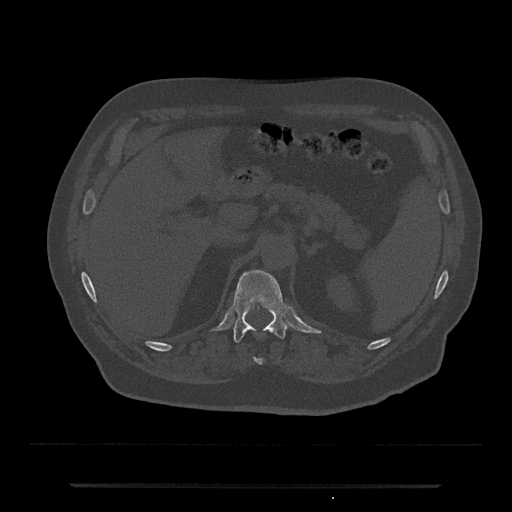
CT including the spine, one axial slice. Position 601 of 797 along the scan axis. 120 kVp. Bone window (W 1800 / L 400 HU). 0.5 mm slice thickness. 512 × 512 image matrix. Male patient, age 80 years. Case-level facts recorded for this patient, not image findings: primary cancer: prostate; vertebrae with lytic lesions (as recorded): L1, T11.
Structures marked on this image (semi-automatic segmentation, software-assisted and operator-edited):
- T11 vertebra: box from (x=254, y=358) to (x=263, y=364) px
- T12 vertebra: (x=233, y=270)–(x=288, y=343)